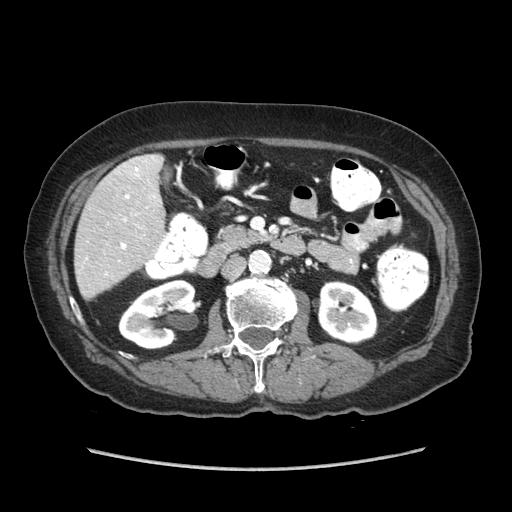
Contrast-enhanced abdominal CT (liver protocol), one axial slice; position 23 of 89 along the scan axis; reconstruction kernel STANDARD; soft-tissue window (W 400 / L 40 HU); 512 × 512 image matrix, field of view 360 × 360 mm. From the clinical record (not read from this slice): diagnosis: hepatocellular carcinoma (patient treated with transarterial chemoembolisation; whether this scan precedes or follows treatment is not stated here); TNM stage (as recorded): Stage-IIIA; Child-Pugh class: A; tumour size: 11 cm.
Outlined on this slice (semi-automatically segmented with operator editing):
- liver parenchyma outside the tumour (the mass and vessels are separate outlines, so this box may not span the whole liver): bounding box (x1, y1, x2, y2) in pixels: (74, 154, 164, 300)
- liver vessels: (105, 157, 155, 275)